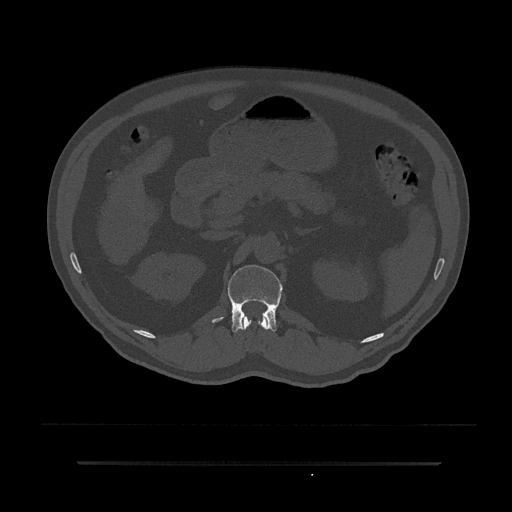
CT including the spine, one axial slice. Slice 166 of 797 in the series (ordered by position). Reconstruction kernel Br40s/3. 120 kVp. Bone window (W 1800 / L 400 HU). 0.5 mm slice thickness. 512 × 512 image matrix, field of view 464 × 464 mm. Patient: male, 59 years. From the clinical record (not read from this slice): primary cancer: bile ducts; vertebrae with lytic lesions (as recorded): T10.
Outlined on this slice (semi-automatically segmented with operator editing):
- L1 vertebra: bounding box [x1, y1, x2, y2] px = [212, 265, 283, 333]
- T12 vertebra: [241, 316, 268, 330]